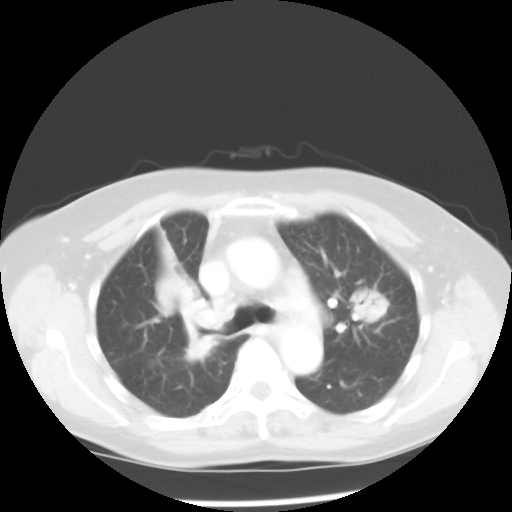
Chest CT, one axial slice. Reconstruction kernel STANDARD. 100 kVp. Lung window (W 1500 / L -600 HU). 5 mm slice thickness. 512 × 512 image matrix, field of view 328 × 328 mm. Female patient, age 60 years. Case-level facts recorded for this patient, not image findings: clinical TNM (as recorded): T2 N1 M1a.
Outlined on this slice (rectangle marked by the reading radiologist):
- lung tumour (recorded histology: adenocarcinoma): bounding box (x1, y1, x2, y2) in pixels: (151, 243, 222, 368)